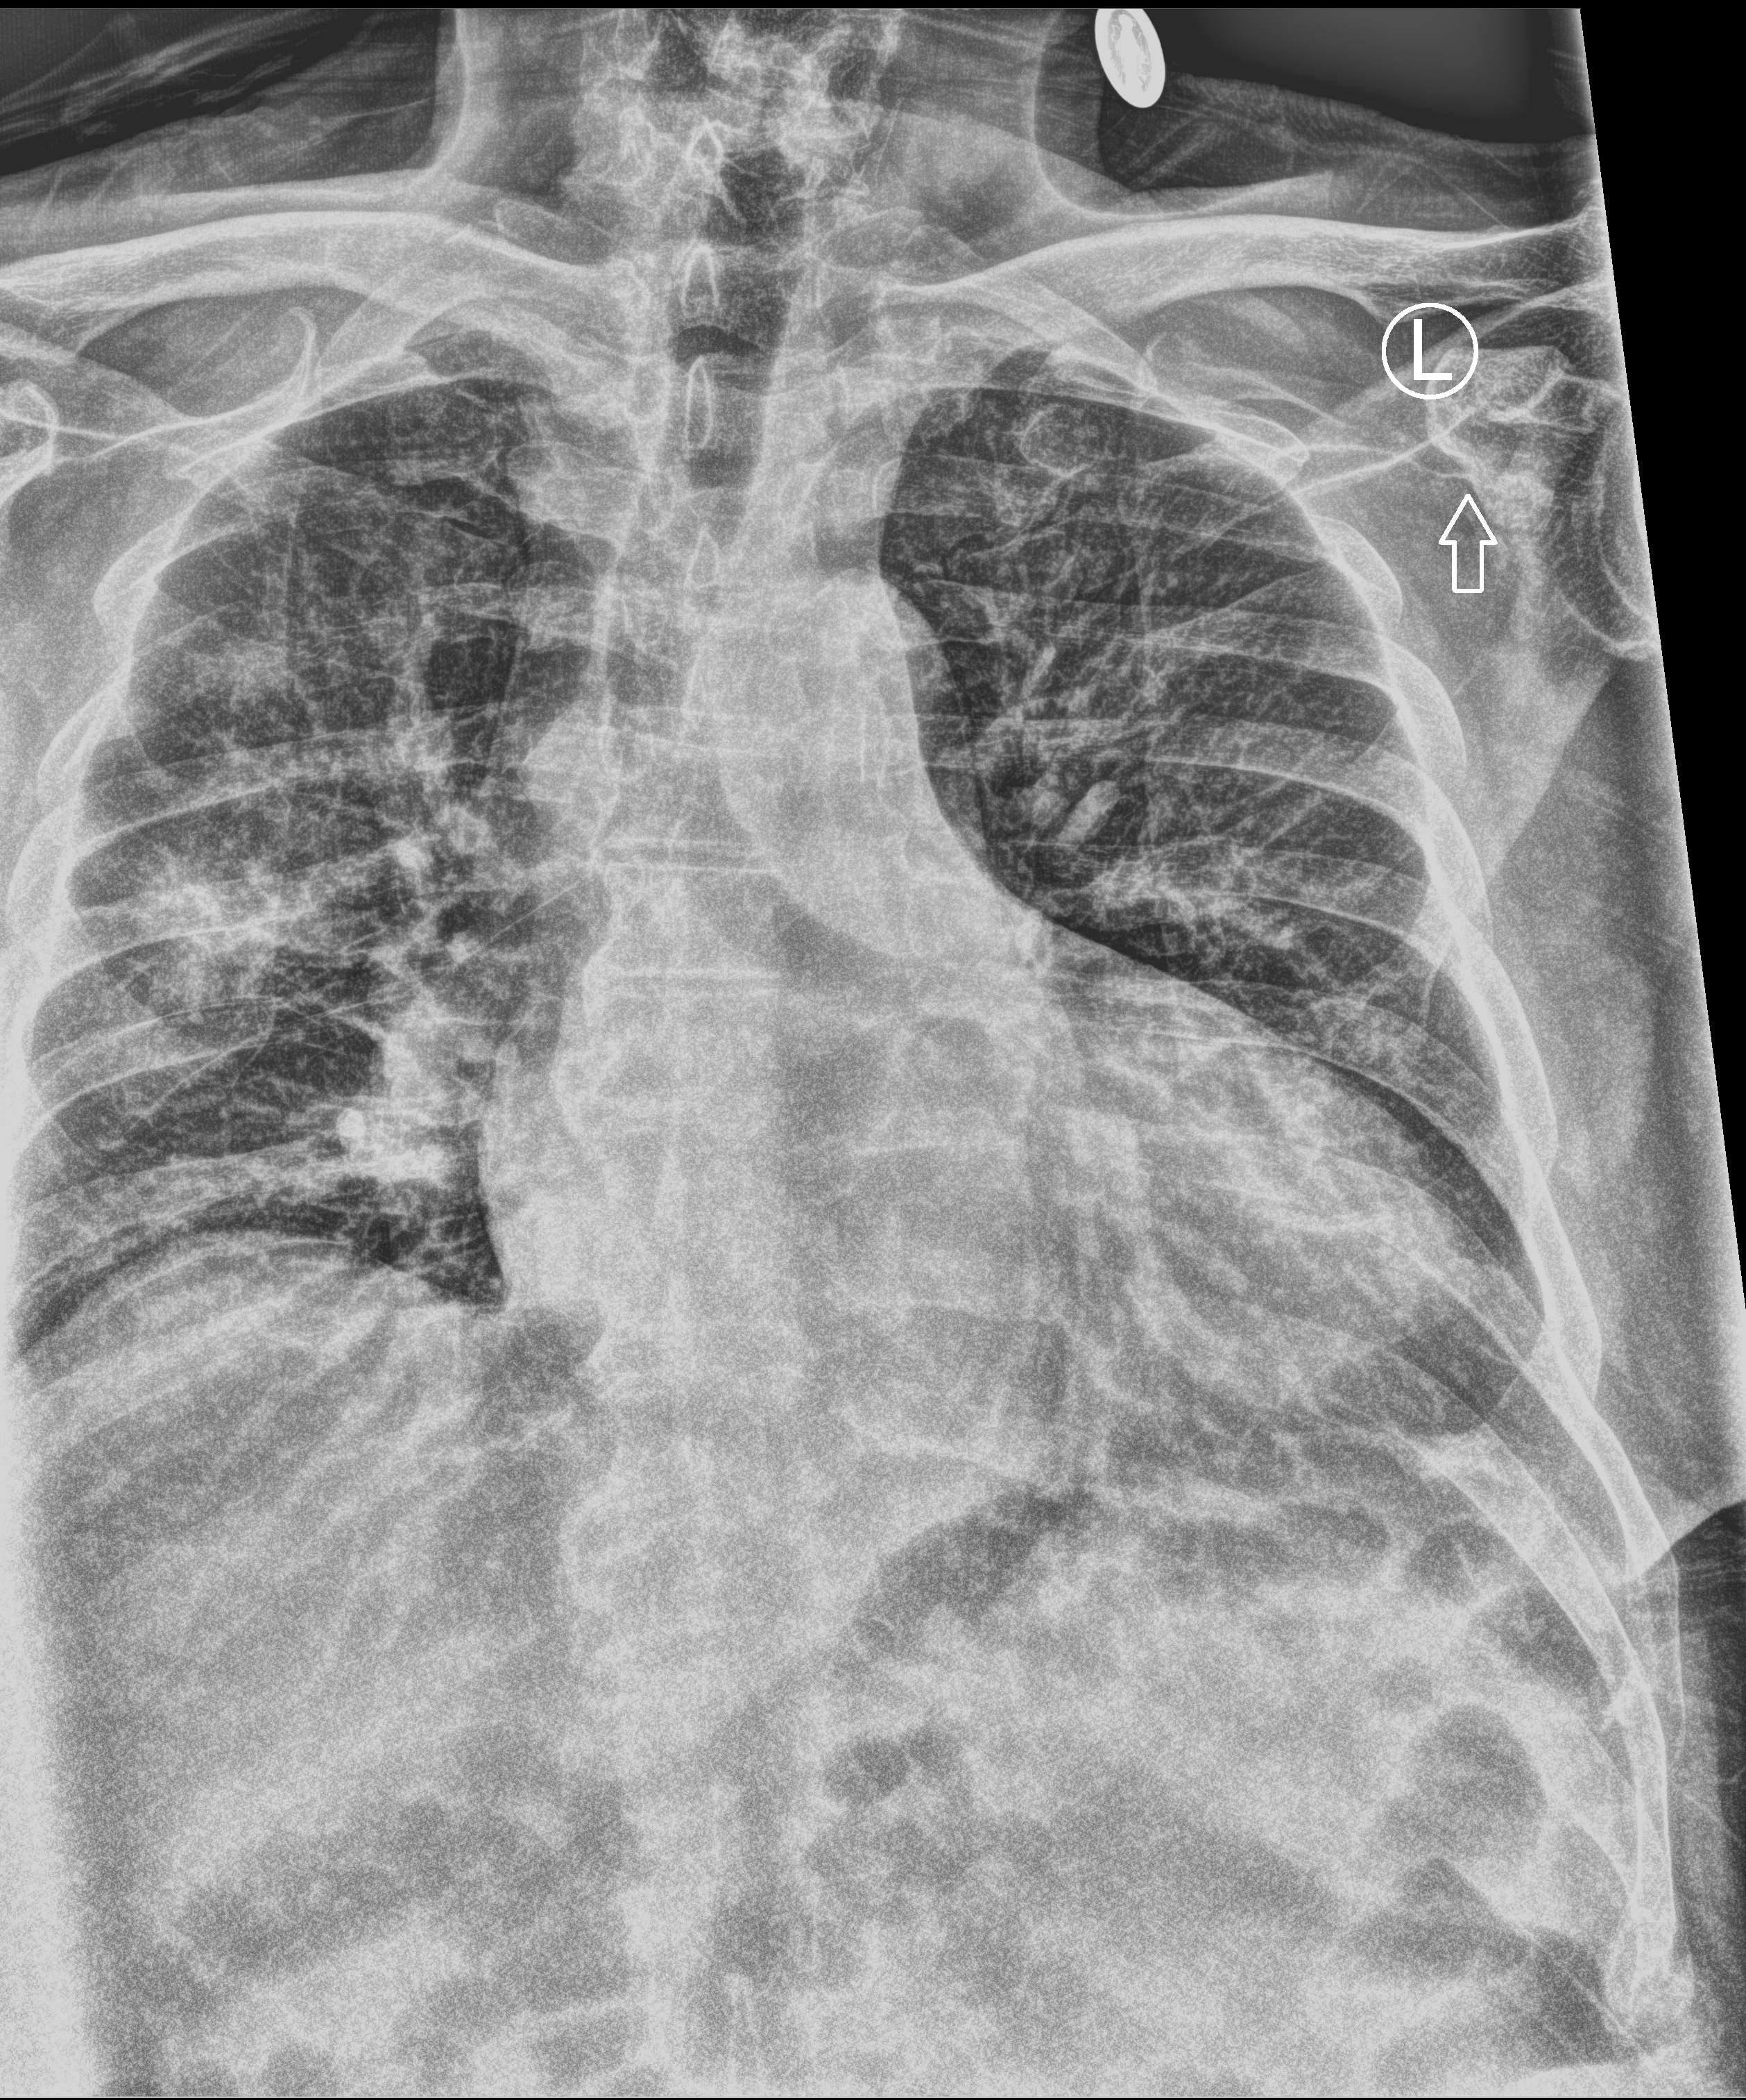
Bedside chest radiograph (computed radiography); anteroposterior (AP) projection. Male patient hospitalised with COVID-19, age 75–90 years.
Hospital-stay facts (about this admission, not read from this image; timing relative to this image not recorded): mechanically ventilated during this hospital stay: no.